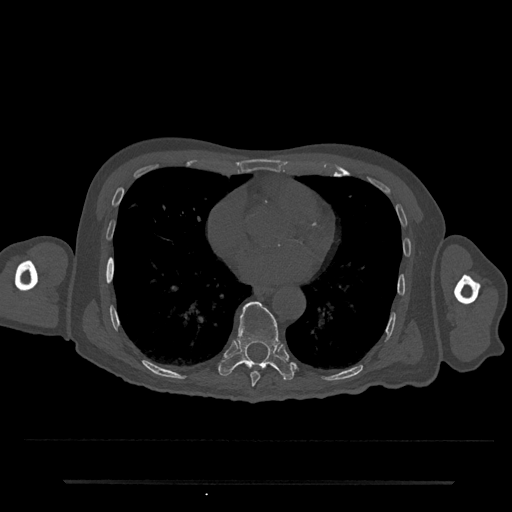
CT including the spine, one axial slice. Slice 384 of 797 in the series (ordered by position). Bone window (W 1800 / L 400 HU). 0.5 mm slice thickness. 512 × 512 image matrix, field of view 427 × 427 mm. Male patient, age 74 years. Case-level facts recorded for this patient, not image findings: primary cancer: prostate.
Structures marked on this image (semi-automatic segmentation, software-assisted and operator-edited):
- T8 vertebra: bounding box (x1, y1, x2, y2) in pixels: (250, 371, 261, 386)
- T9 vertebra: (218, 301, 295, 380)